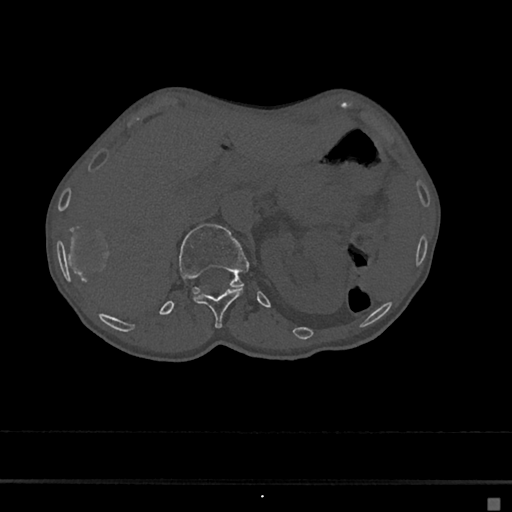
CT including the spine, one axial slice; slice 99 of 797 in the series (ordered by position); reconstruction kernel Br40s/3; 120 kVp; bone window (W 1800 / L 400 HU); 0.5 mm slice thickness; 512 × 512 image matrix, field of view 360 × 360 mm. Female patient, age 68 years. From the clinical record (not read from this slice): primary cancer: renal.
Outlined on this slice (semi-automatically segmented with operator editing):
- L1 vertebra: bounding box <178,224,251,294> (left, top, right, bottom; pixels)
- T12 vertebra: <194,288,243,329>